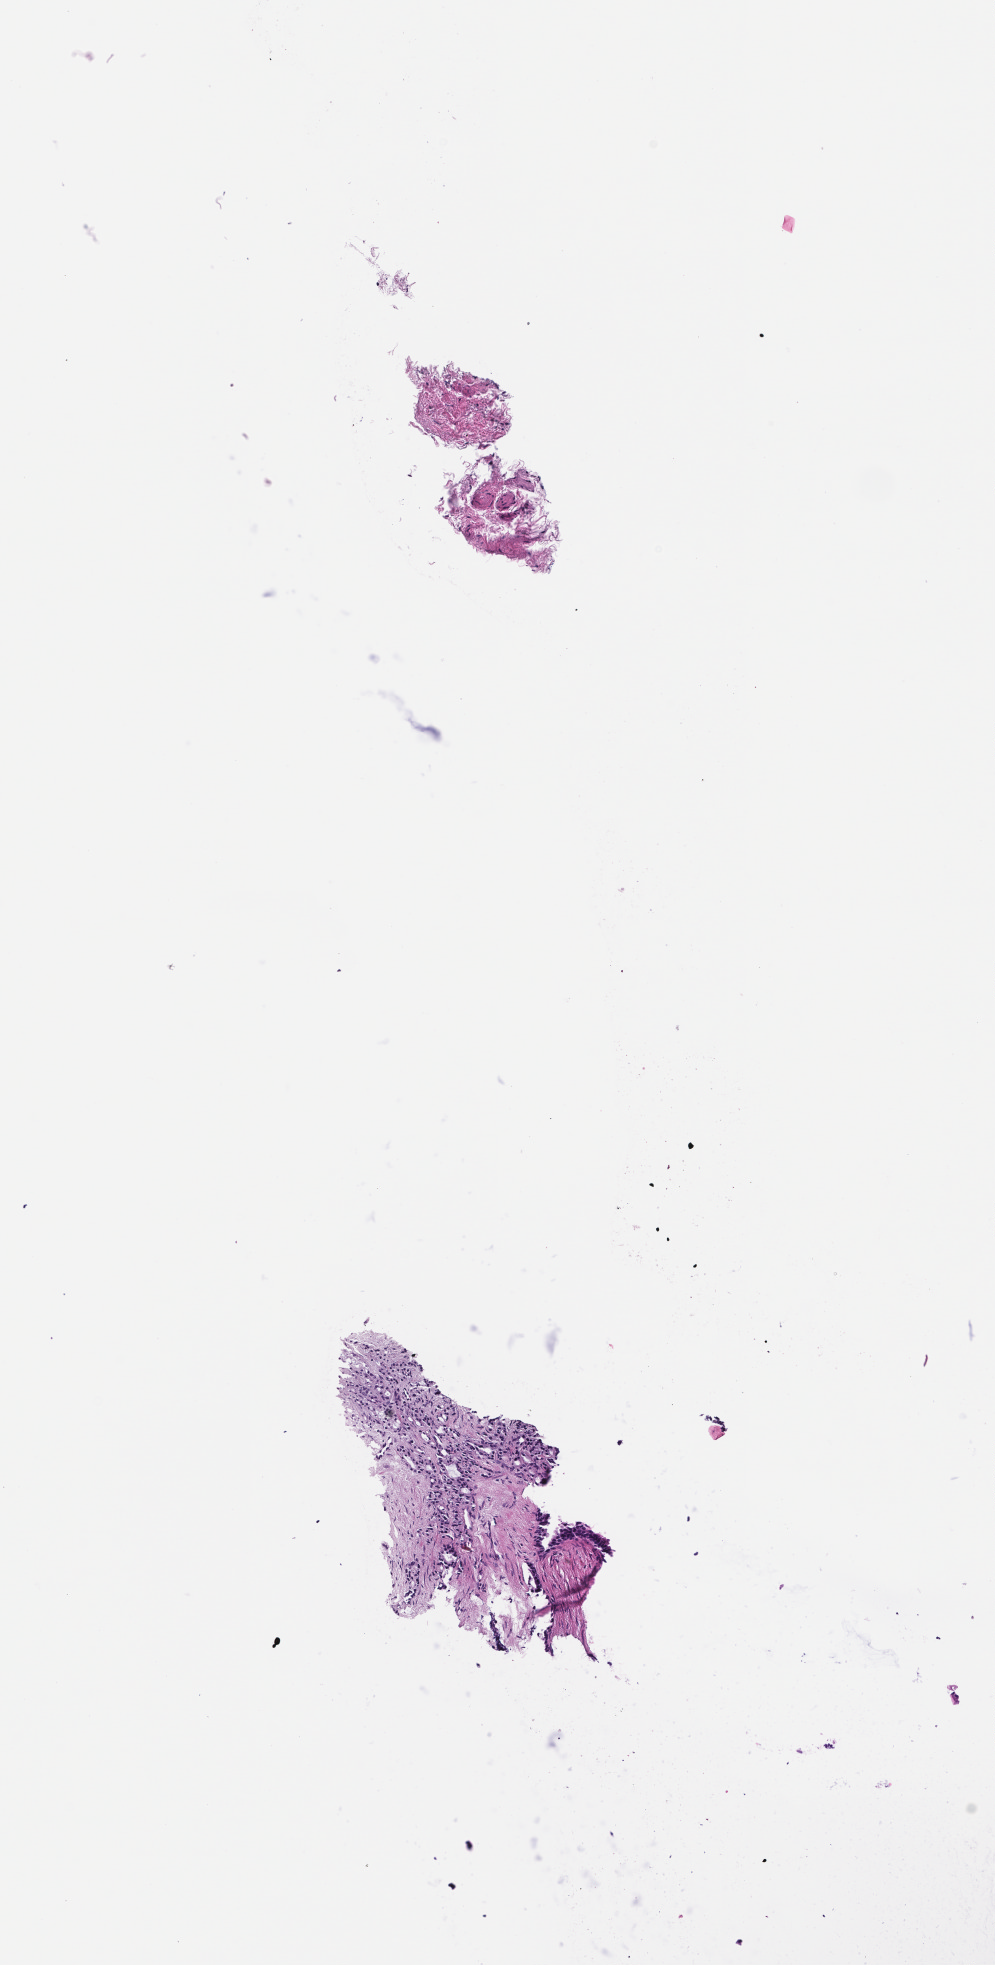
Whole-slide image, hematoxylin and eosin (H&E) stain, shown as a low-resolution overview of the whole scanned area (about 2.0 x 4.0 mm). FFPE section. Tissue site: prostate. Specimen time point: archival tissue. Patient sex: male.
This section: primary tumour tissue. Diagnosis: Prostate Carcinoma.